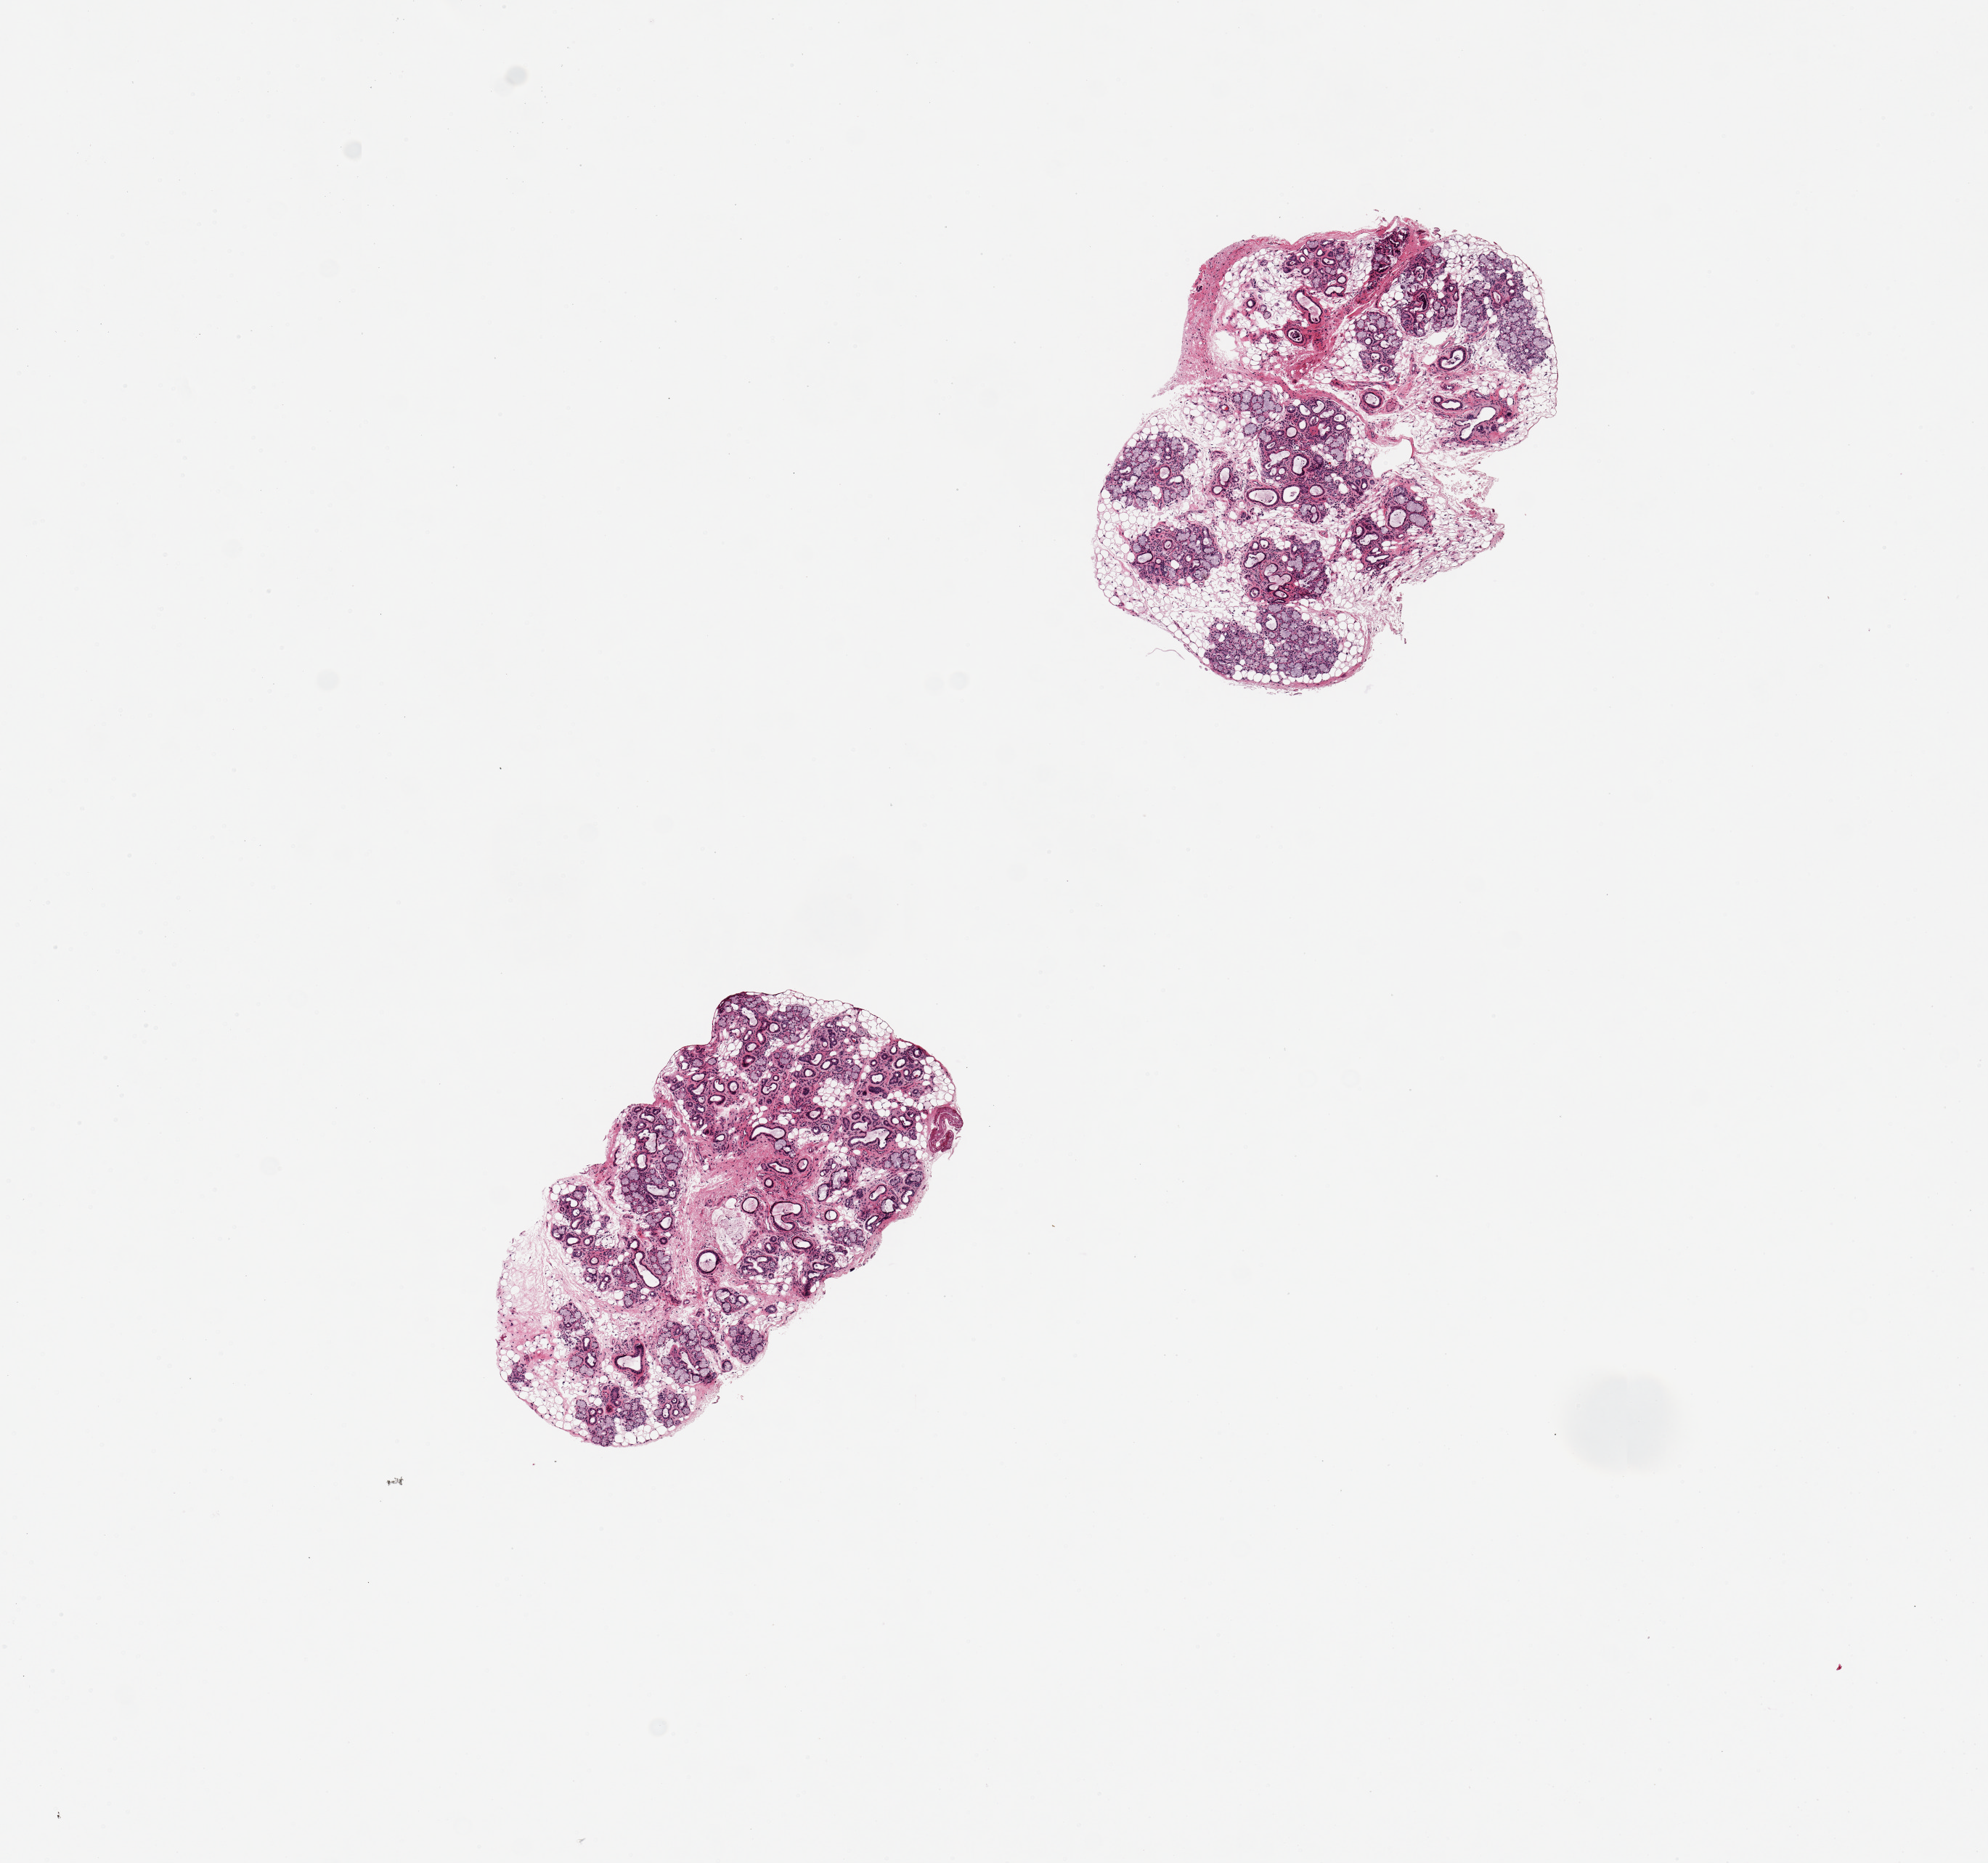
Digitized haematoxylin and eosin-stained section — low-resolution overview of the scanned area, about 10.8 x 10.1 mm. PAXgene-fixed, paraffin-embedded tissue. Section of minor salivary gland (target tissue). Donor tissue sample. Donor: male.
Pathologist's review note for this sample: 2 pieces, 3x2 & 3x2mm; 2 well dissected glandular clusters with 40-50% internal adipose; moderate duct dilatation and gland atrophy.